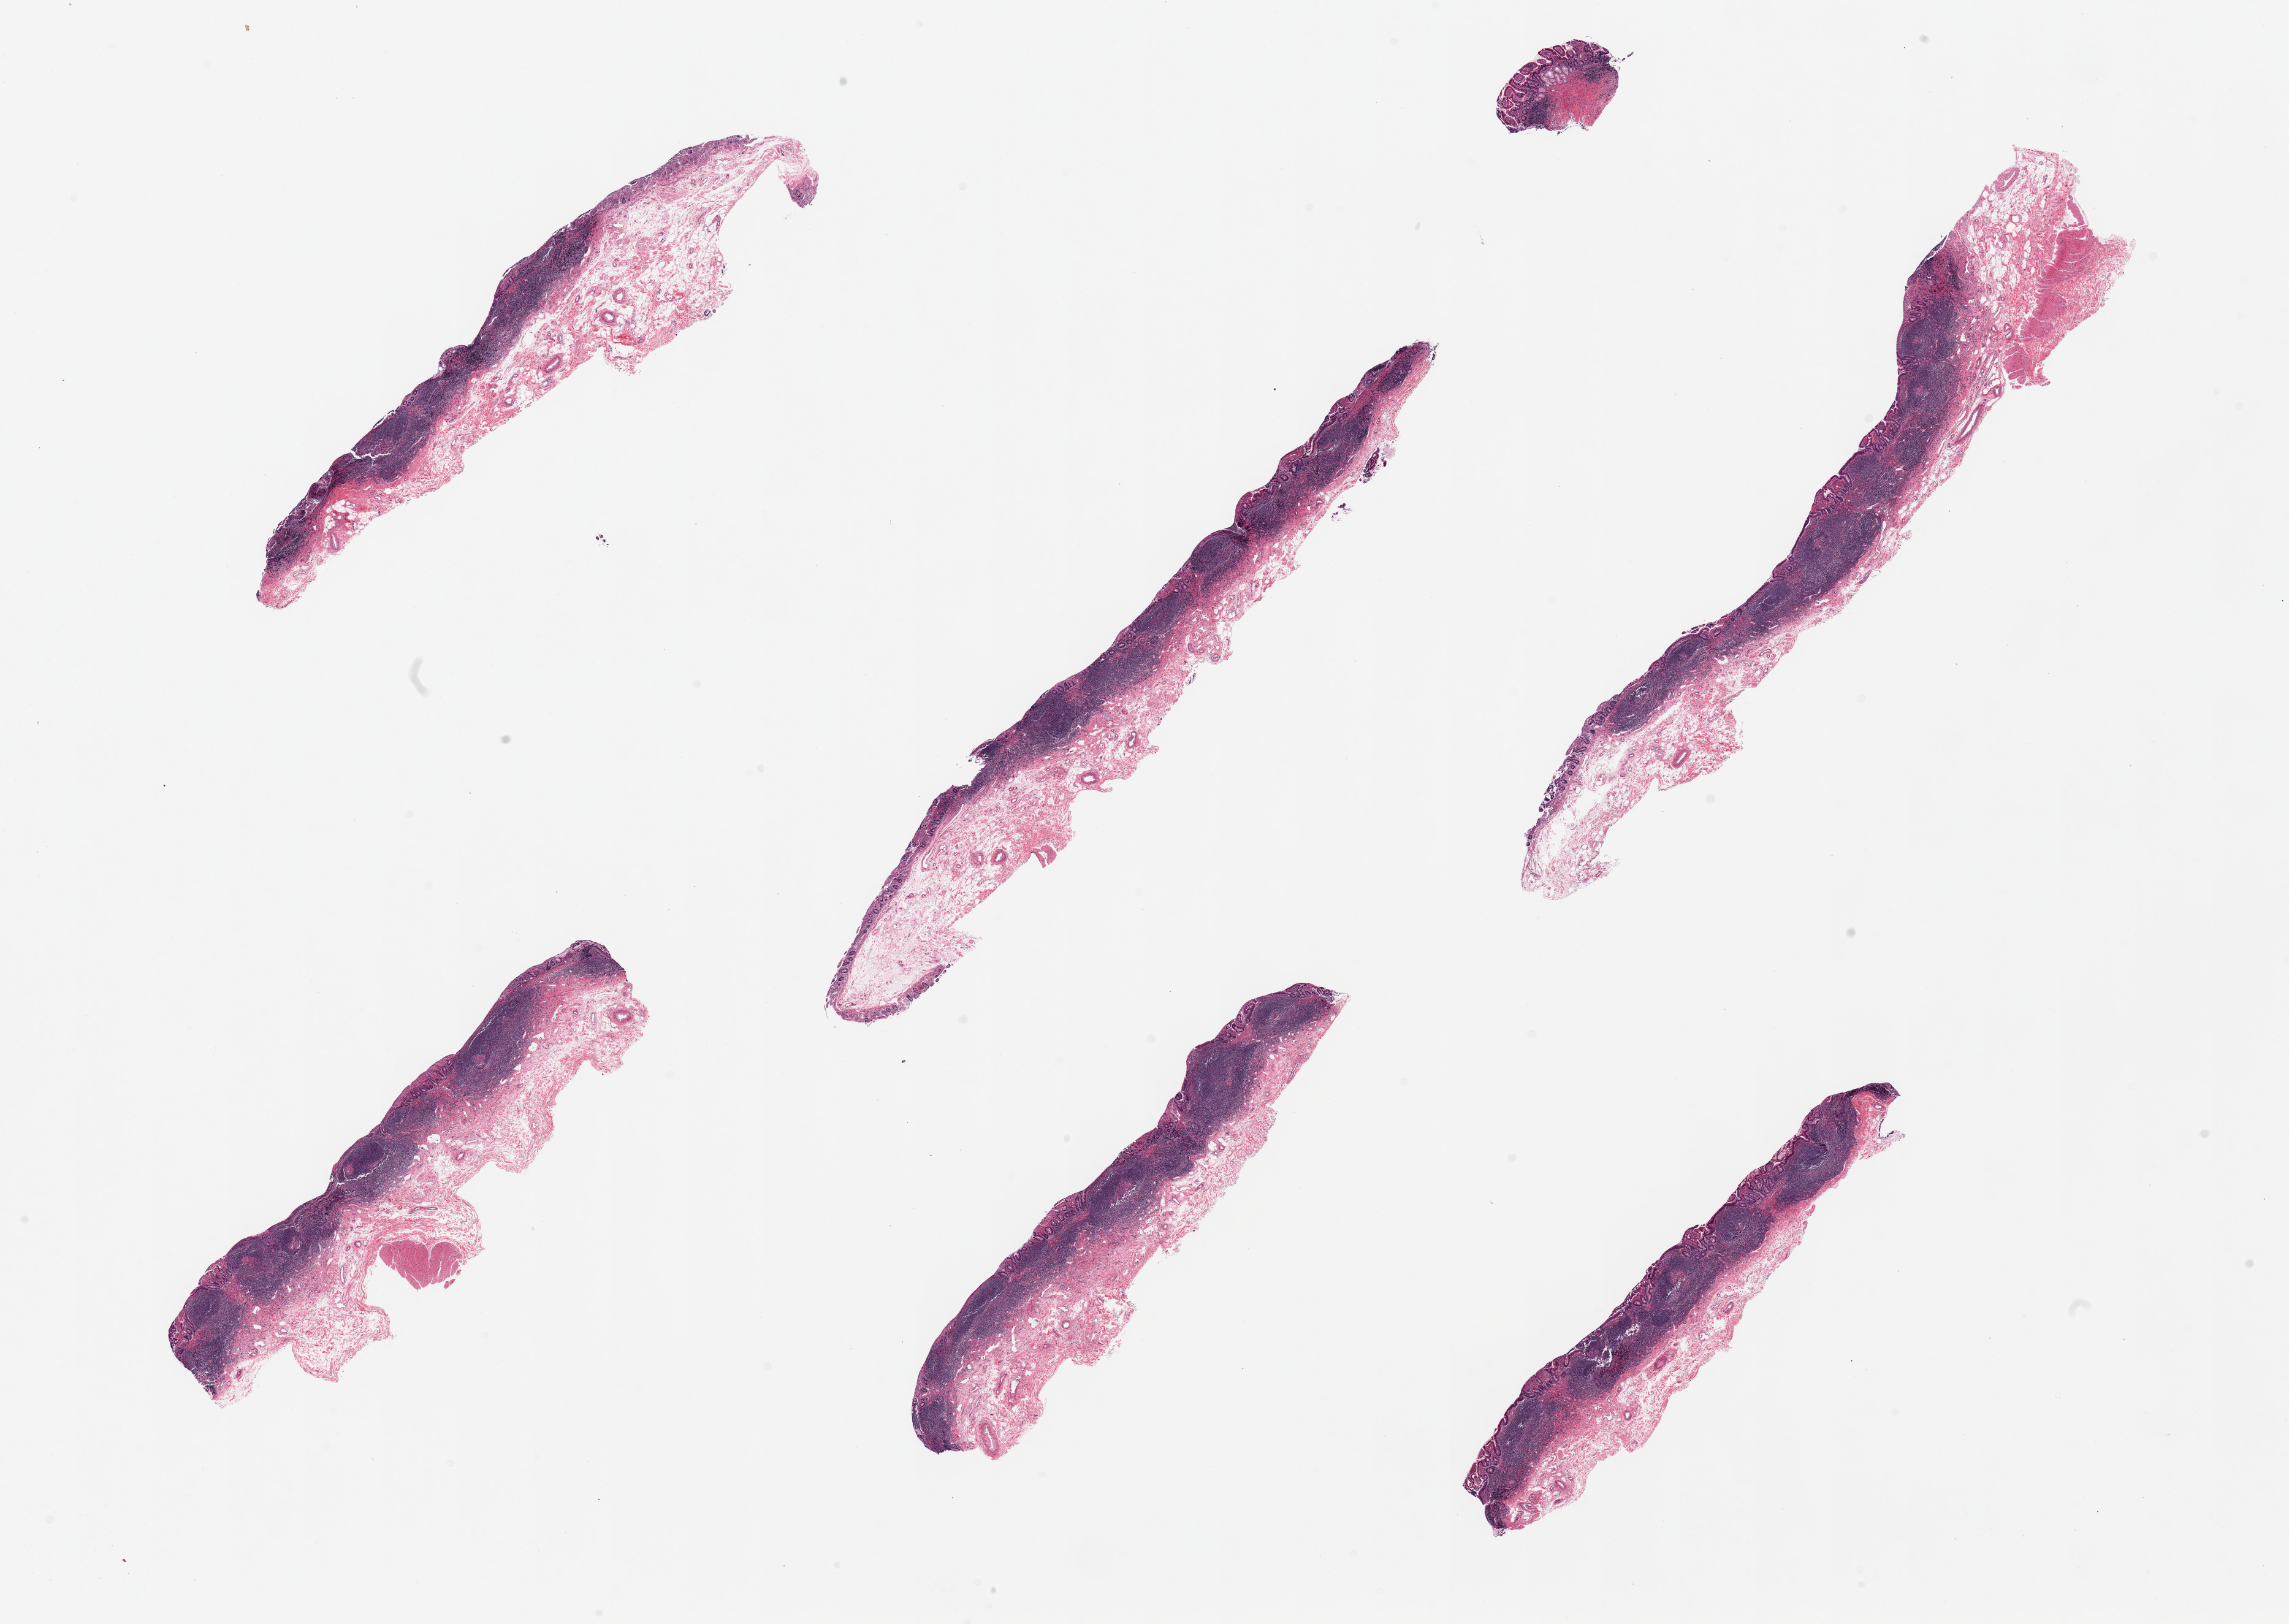
H&E whole-slide image — shown as a low-resolution overview of the whole scanned area (about 29.5 x 21.0 mm, from a 20x scan); PAXgene-fixed paraffin-embedded (PFPE) section; section of ileum (target tissue); tissue donor sample.
- pathologist's review note for this sample: 6 pieces, well preserved, abundant lymphoidd aggregates up to ~50% total tissue